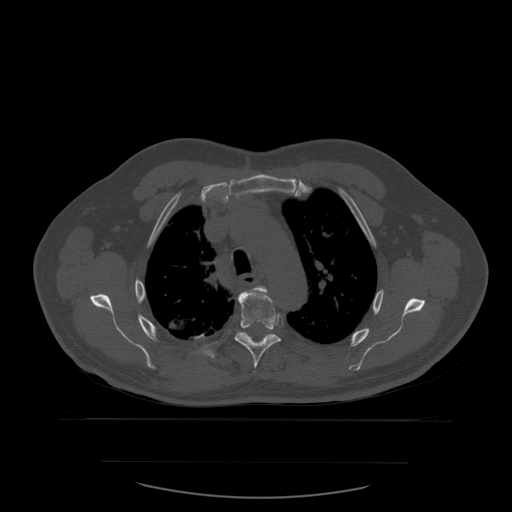
CT including the spine, one axial slice; position 424 of 590 along the scan axis; bone window (W 1800 / L 400 HU); 512 × 512 image matrix, field of view 479 × 479 mm. Patient age 71 years. From the clinical record (not read from this slice): primary cancer: lung; vertebrae with lytic lesions (as recorded): T1, T2, L5, S1.
Annotated regions visible in this slice (semi-automatically segmented with operator editing):
- T4 vertebra: bounding box <246,286,268,294> (left, top, right, bottom; pixels)
- T5 vertebra: <235,291,281,369>
- T6 vertebra: <241,332,273,341>